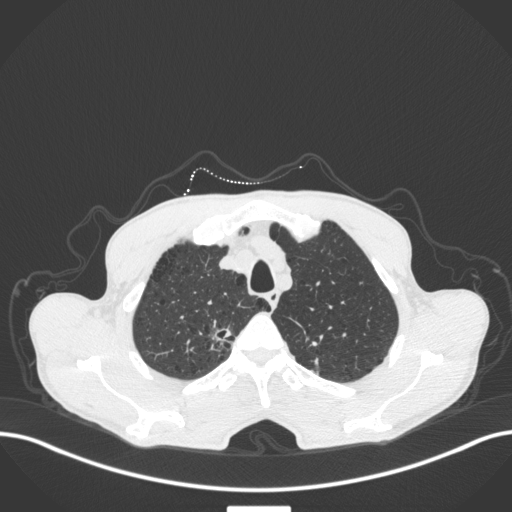
Chest CT, one axial slice; position 362 of 445 along the scan axis; reconstruction kernel B31f; lung window (W 1500 / L -600 HU); 1 mm slice thickness; 512 × 512 image matrix, field of view 400 × 400 mm. Male patient, age 70 years. Case-level facts recorded for this patient, not image findings: clinical TNM (as recorded): T1a N0 M0; histopathological grade: G1-2.
Annotated regions visible in this slice (rectangle marked by the reading radiologist):
- lung tumour (recorded histology: adenocarcinoma): bounding box [x1, y1, x2, y2] px = [208, 320, 233, 345]